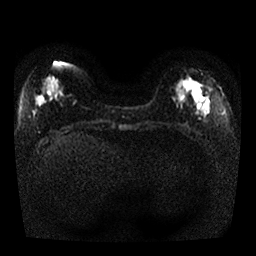
Breast MRI, one axial slice. Diffusion-weighted series; image 2 of 4 stored at this slice position (different b-values; order by instance number). 1.5 T. 4 mm slice thickness. 256 × 256 image matrix, field of view 330 × 330 mm. Female patient.
Annotated regions visible in this slice (manually delineated by an expert):
- tumour on diffusion-weighted imaging: bounding box <184,83,192,92> (left, top, right, bottom; pixels)